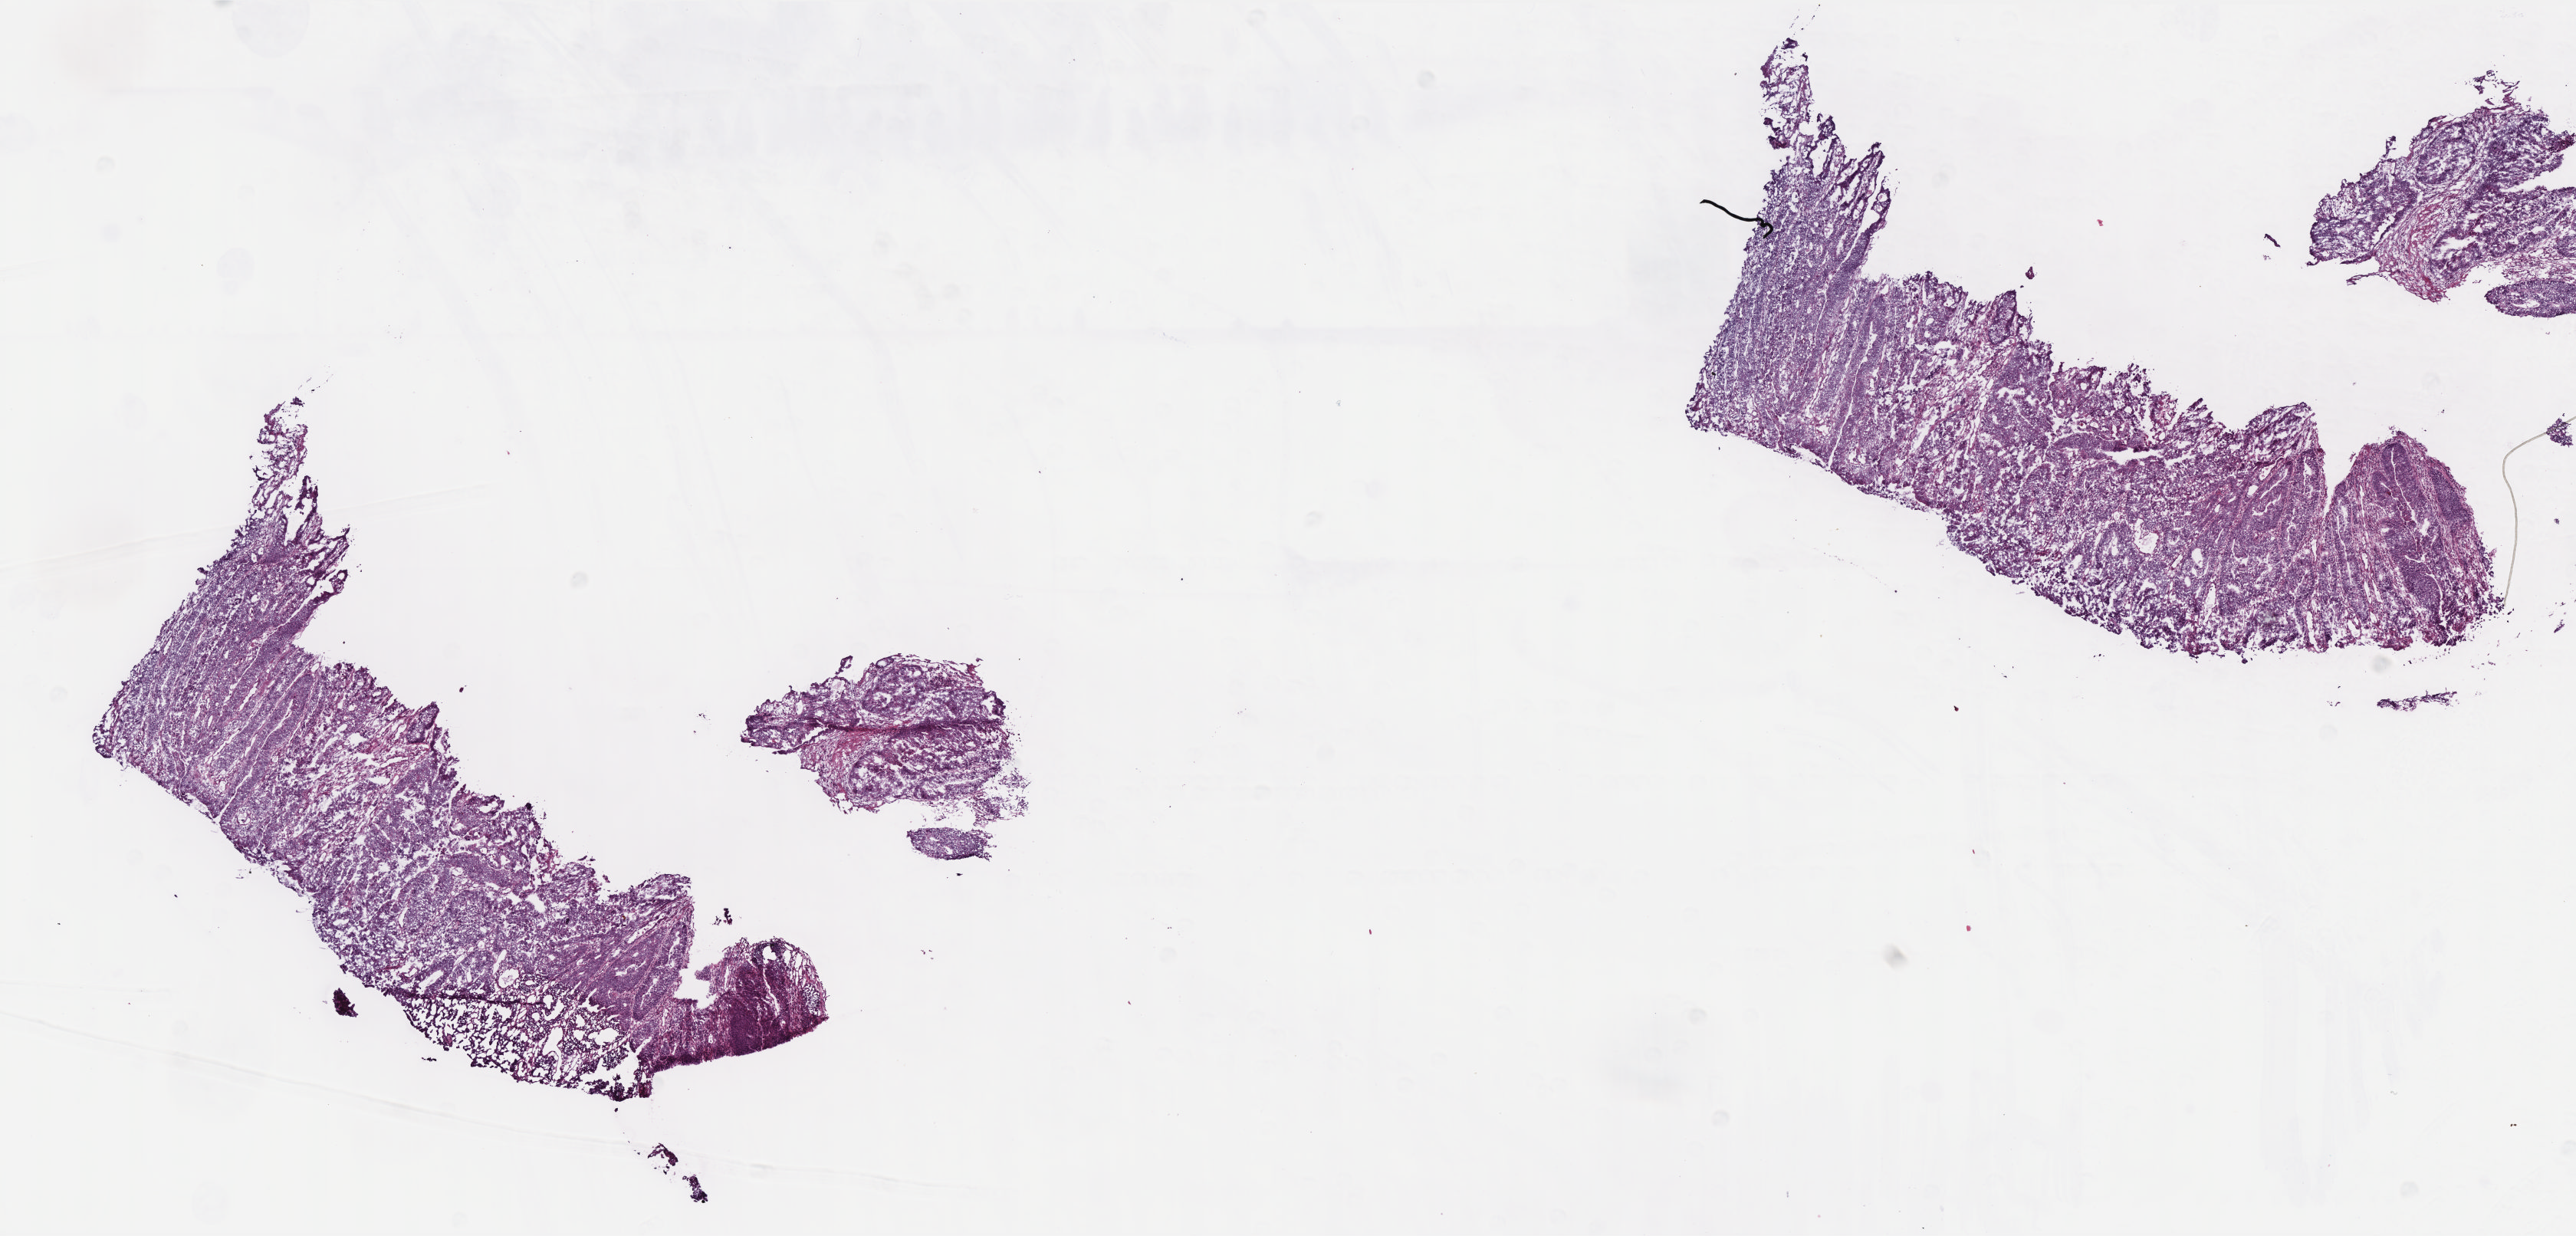
Whole-slide histology image, H&E, a low-resolution overview of the entire scanned area, about 13.5 x 6.5 mm (from a 40x scan); frozen section; rectum, primary tumour sample. Female patient; age at initial diagnosis 68 years. Pathologist review of this section (percent, as recorded): tumour cells 93%, tumour nuclei 90%, normal cells 0%, stromal cells 6%, necrosis 1%. Inflammatory infiltration, as recorded: lymphocyte infiltration 1%, monocyte infiltration 1%, neutrophil infiltration 4%.
• lymph nodes positive (case pathology): 0 of 23 examined
• AJCC pathologic stage: IV
• diagnosis: Adenocarcinoma, NOS